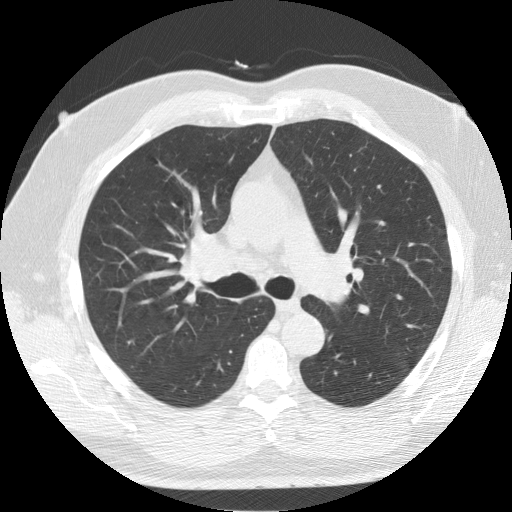
Chest CT (low-dose screening protocol), one axial image; second annual screen; lung window (W 1500 / L -600 HU); standard (soft-tissue) reconstruction kernel (STANDARD). Male, age 64 years at enrolment. Former smoker at enrolment.
Expert-annotated lung lesion, bounding box [x1, y1, x2, y2] px = [169, 224, 256, 303]. The exam's reader record, not a measurement of the box and not confirmed to be the same lesion: non-calcified nodule or mass ≥4 mm, right lower lobe, 7 × 5 mm, smooth margins, soft tissue attenuation, pre-existing on the prior screen: yes; interval growth: no. Participant outcome: lung cancer diagnosed 63 days after this screen — adenocarcinoma, NOS, right upper lobe, poorly differentiated (G3), stage IB (AJCC 6th edition), 37 mm at pathology.